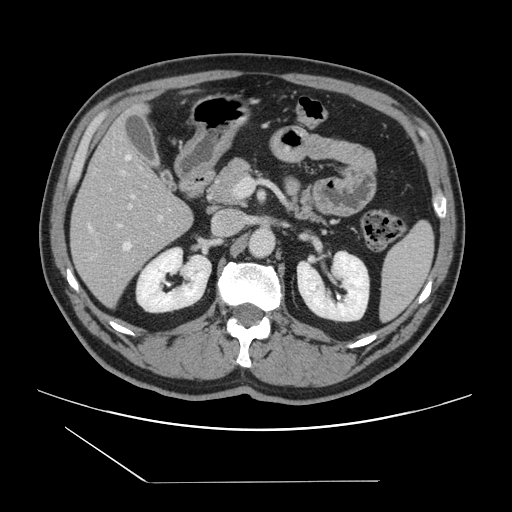
Contrast-enhanced abdominal CT, one axial slice; position 71 of 157 along the scan axis; 120 kVp; intravenous contrast given; soft-tissue window (W 400 / L 40 HU); 2.5 mm slice thickness; 512 × 512 image matrix. Male patient, age 61 years. Case-level facts recorded for this patient, not image findings: diagnosis: colorectal cancer liver metastases, imaged before liver resection; multiple liver metastases: yes; largest metastasis: 5.5 cm; disease in both lobes: yes.
Structures marked on this image (expert manual segmentation):
- hepatic veins: bounding box [x1, y1, x2, y2] px = [89, 155, 134, 250]
- liver: [72, 125, 193, 306]
- planned liver remnant (the part of the liver to remain after resection): [73, 125, 212, 219]
- portal vein (with intrahepatic branches): [119, 170, 163, 226]